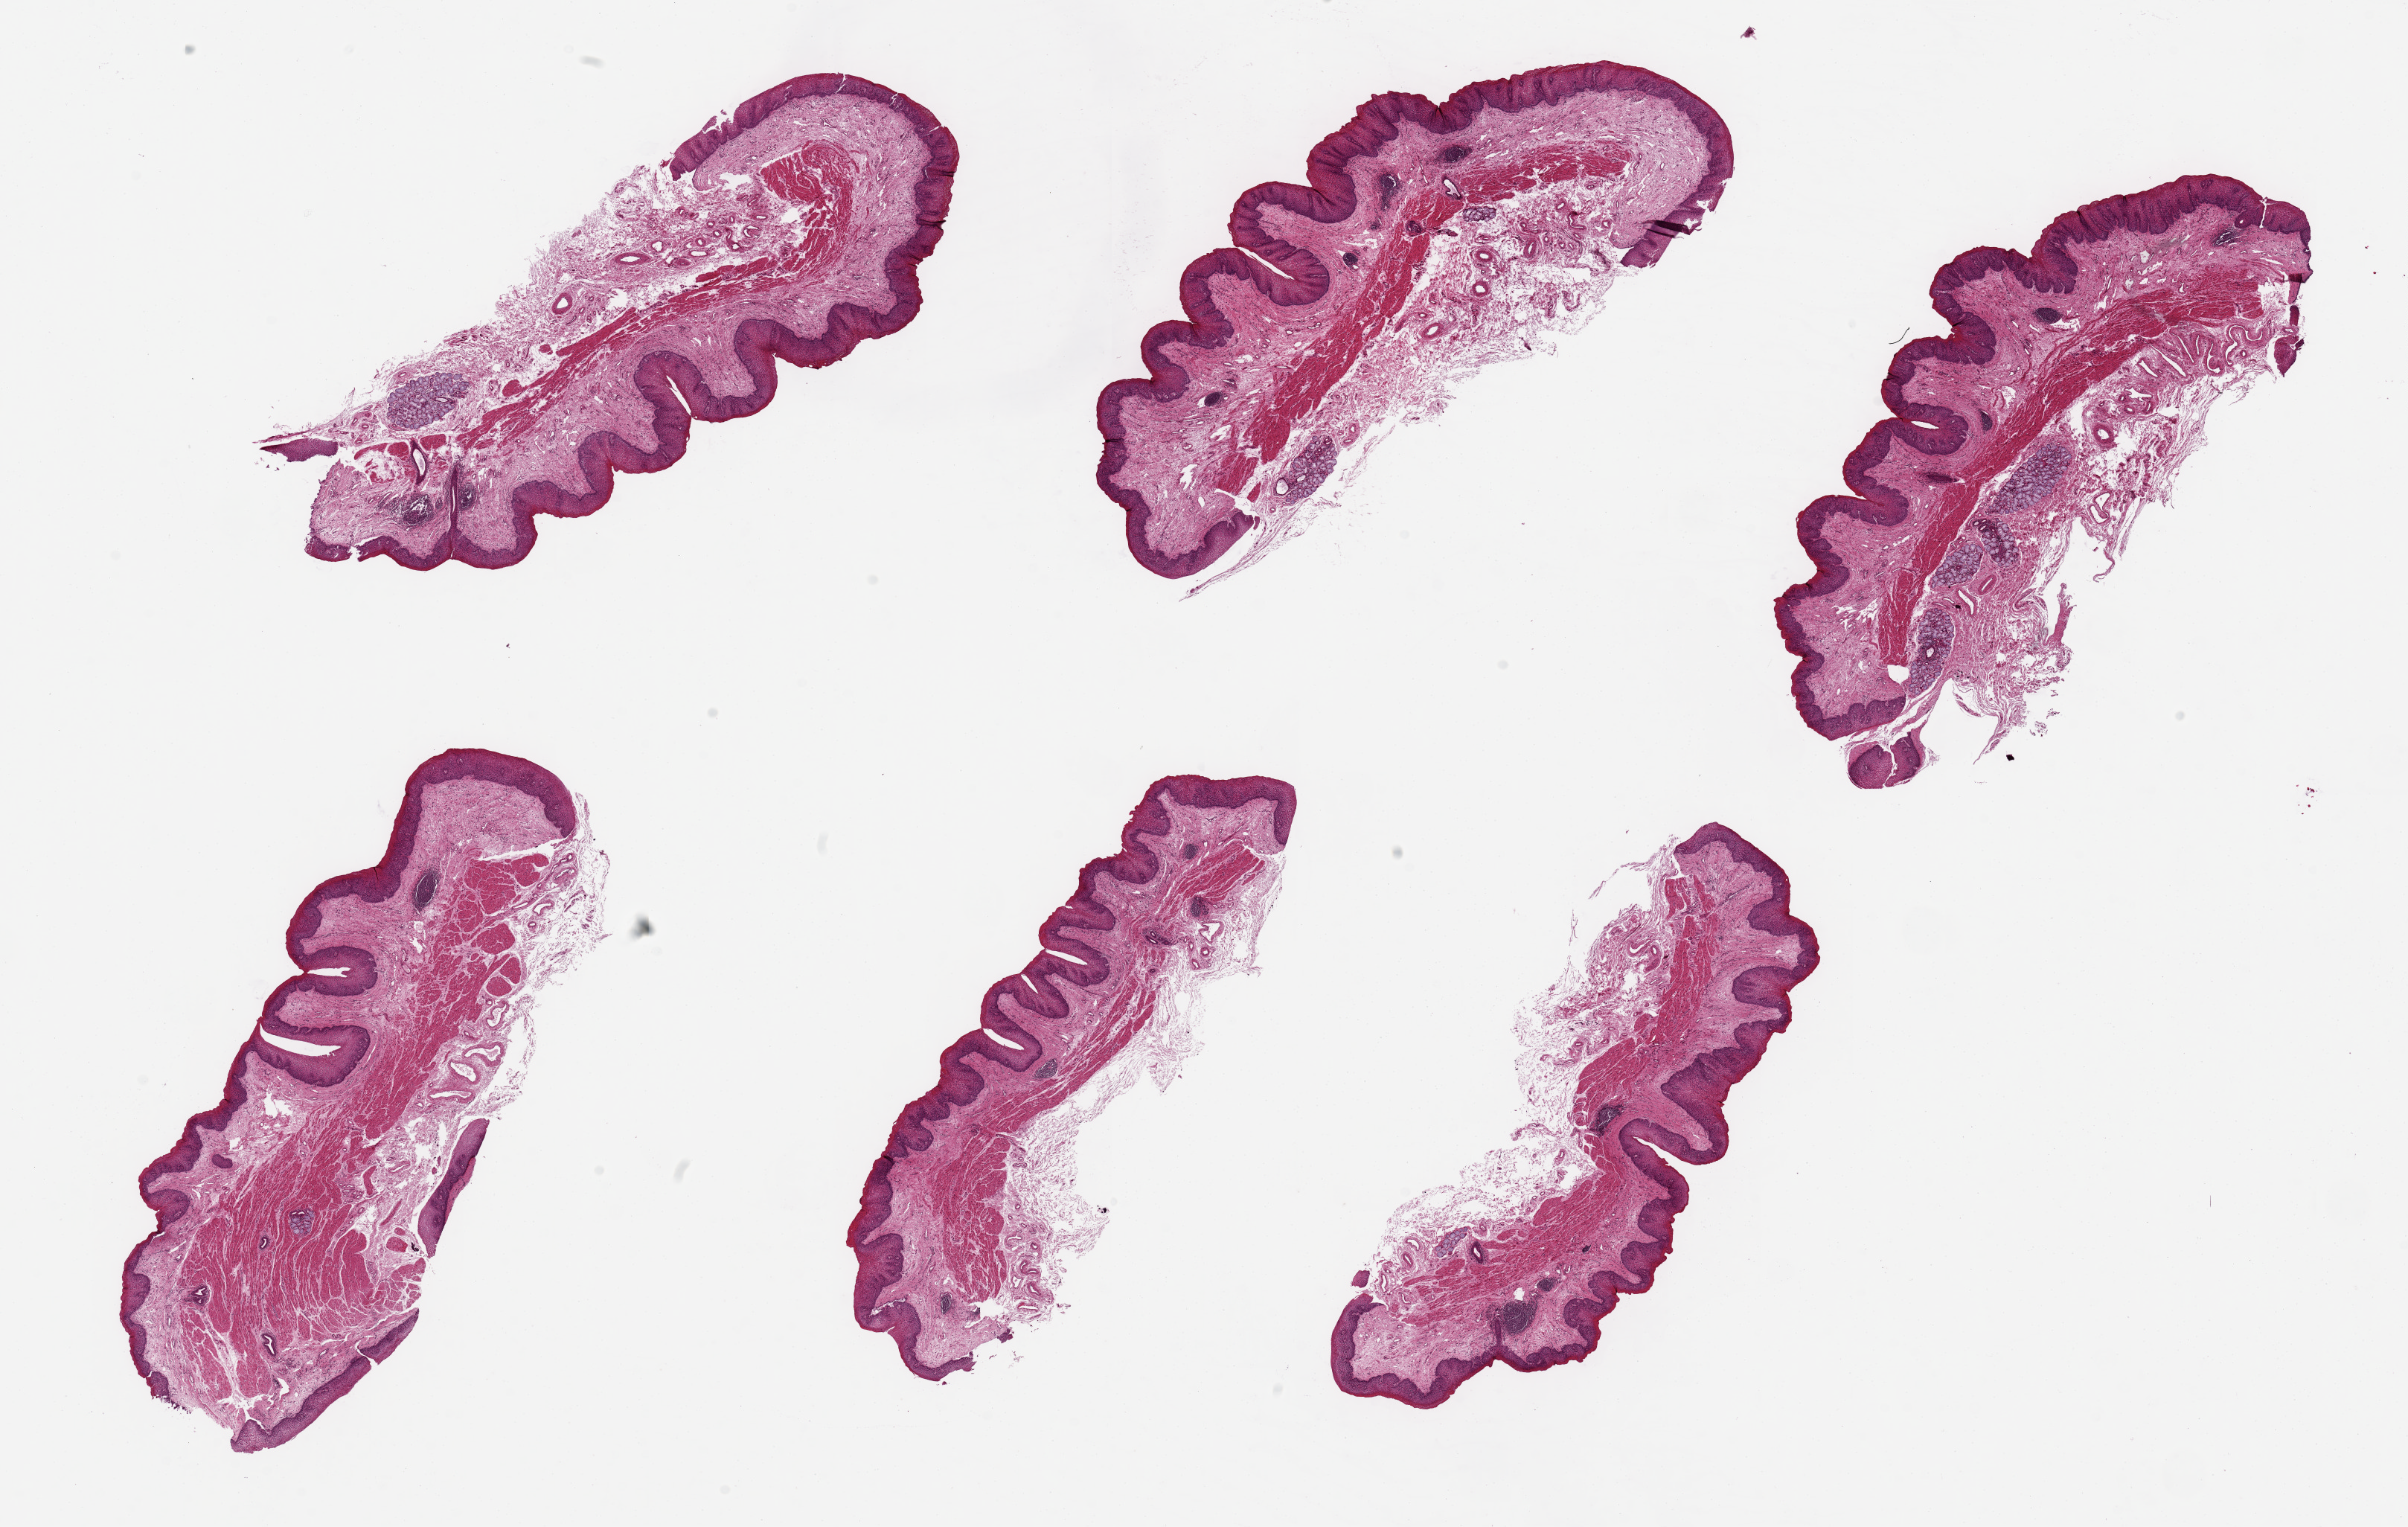
Hematoxylin and eosin (H&E) whole-slide image, shown as a low-resolution overview of the whole scanned area (about 25.6 x 16.2 mm, acquisition: 20x scan); PAXgene-fixed, paraffin-embedded tissue; target tissue: esophageal mucous membrane; donor tissue sample. Donor: male.
- reviewer comment on this tissue sample: 6 pieces up to 8x3.2 mm